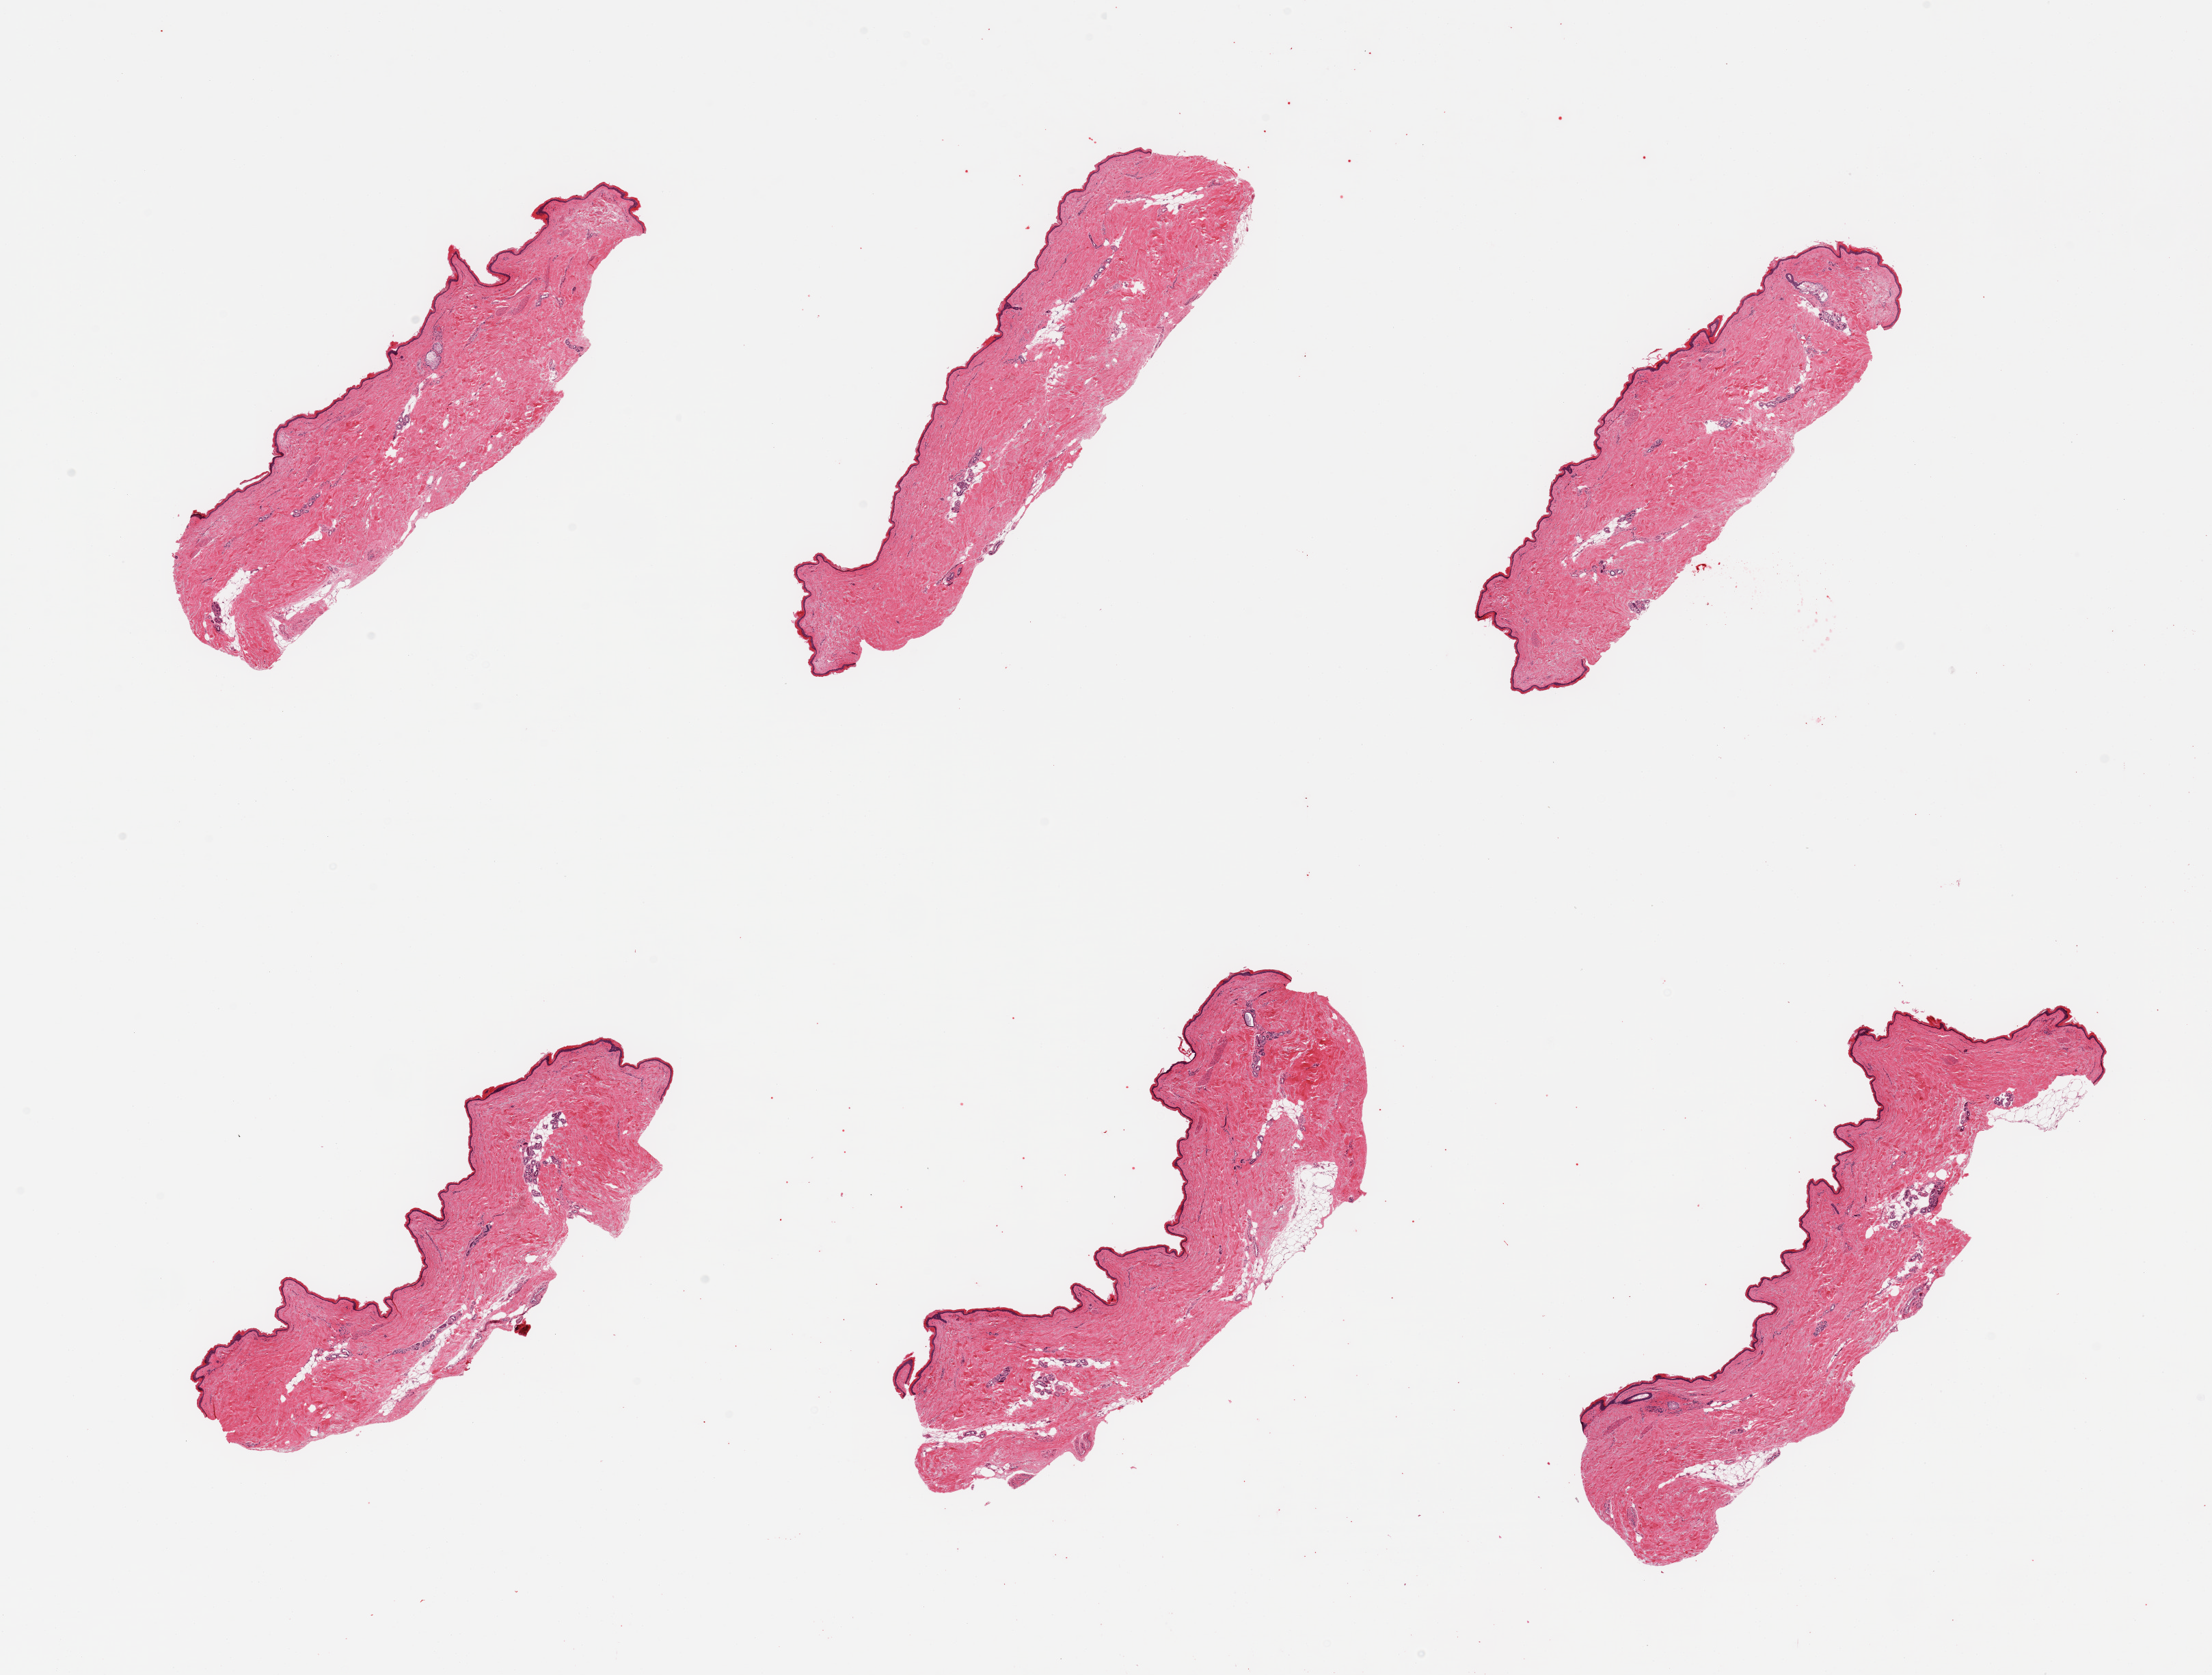
Digitized hematoxylin and eosin (H&E)-stained section, whole scanned area (about 25.6 x 19.4 mm) shown as a low-resolution overview, PAXgene-fixed paraffin-embedded (PFPE) section, sampled site (target tissue): skin of lower leg, donor tissue sample. Donor sex: male.
Pathologist's review note for this sample: 6 pieces; well trimmed; 5% dermal fat.